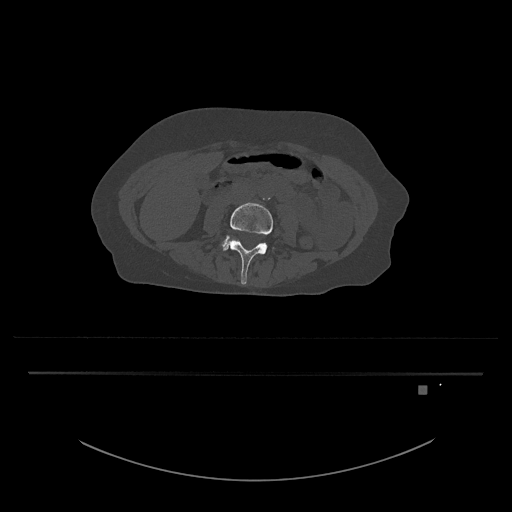
CT including the spine, one axial slice; position 359 of 797 along the scan axis; reconstruction kernel Br40s/3; 120 kVp; bone window (W 1800 / L 400 HU); 0.5 mm slice thickness; 512 × 512 image matrix. Female patient, age 57 years. From the clinical record (not read from this slice): primary cancer: cervical.
Structures marked on this image (semi-automatic segmentation, software-assisted and operator-edited):
- L4 vertebra: bounding box (x1, y1, x2, y2) in pixels: (223, 202, 274, 285)